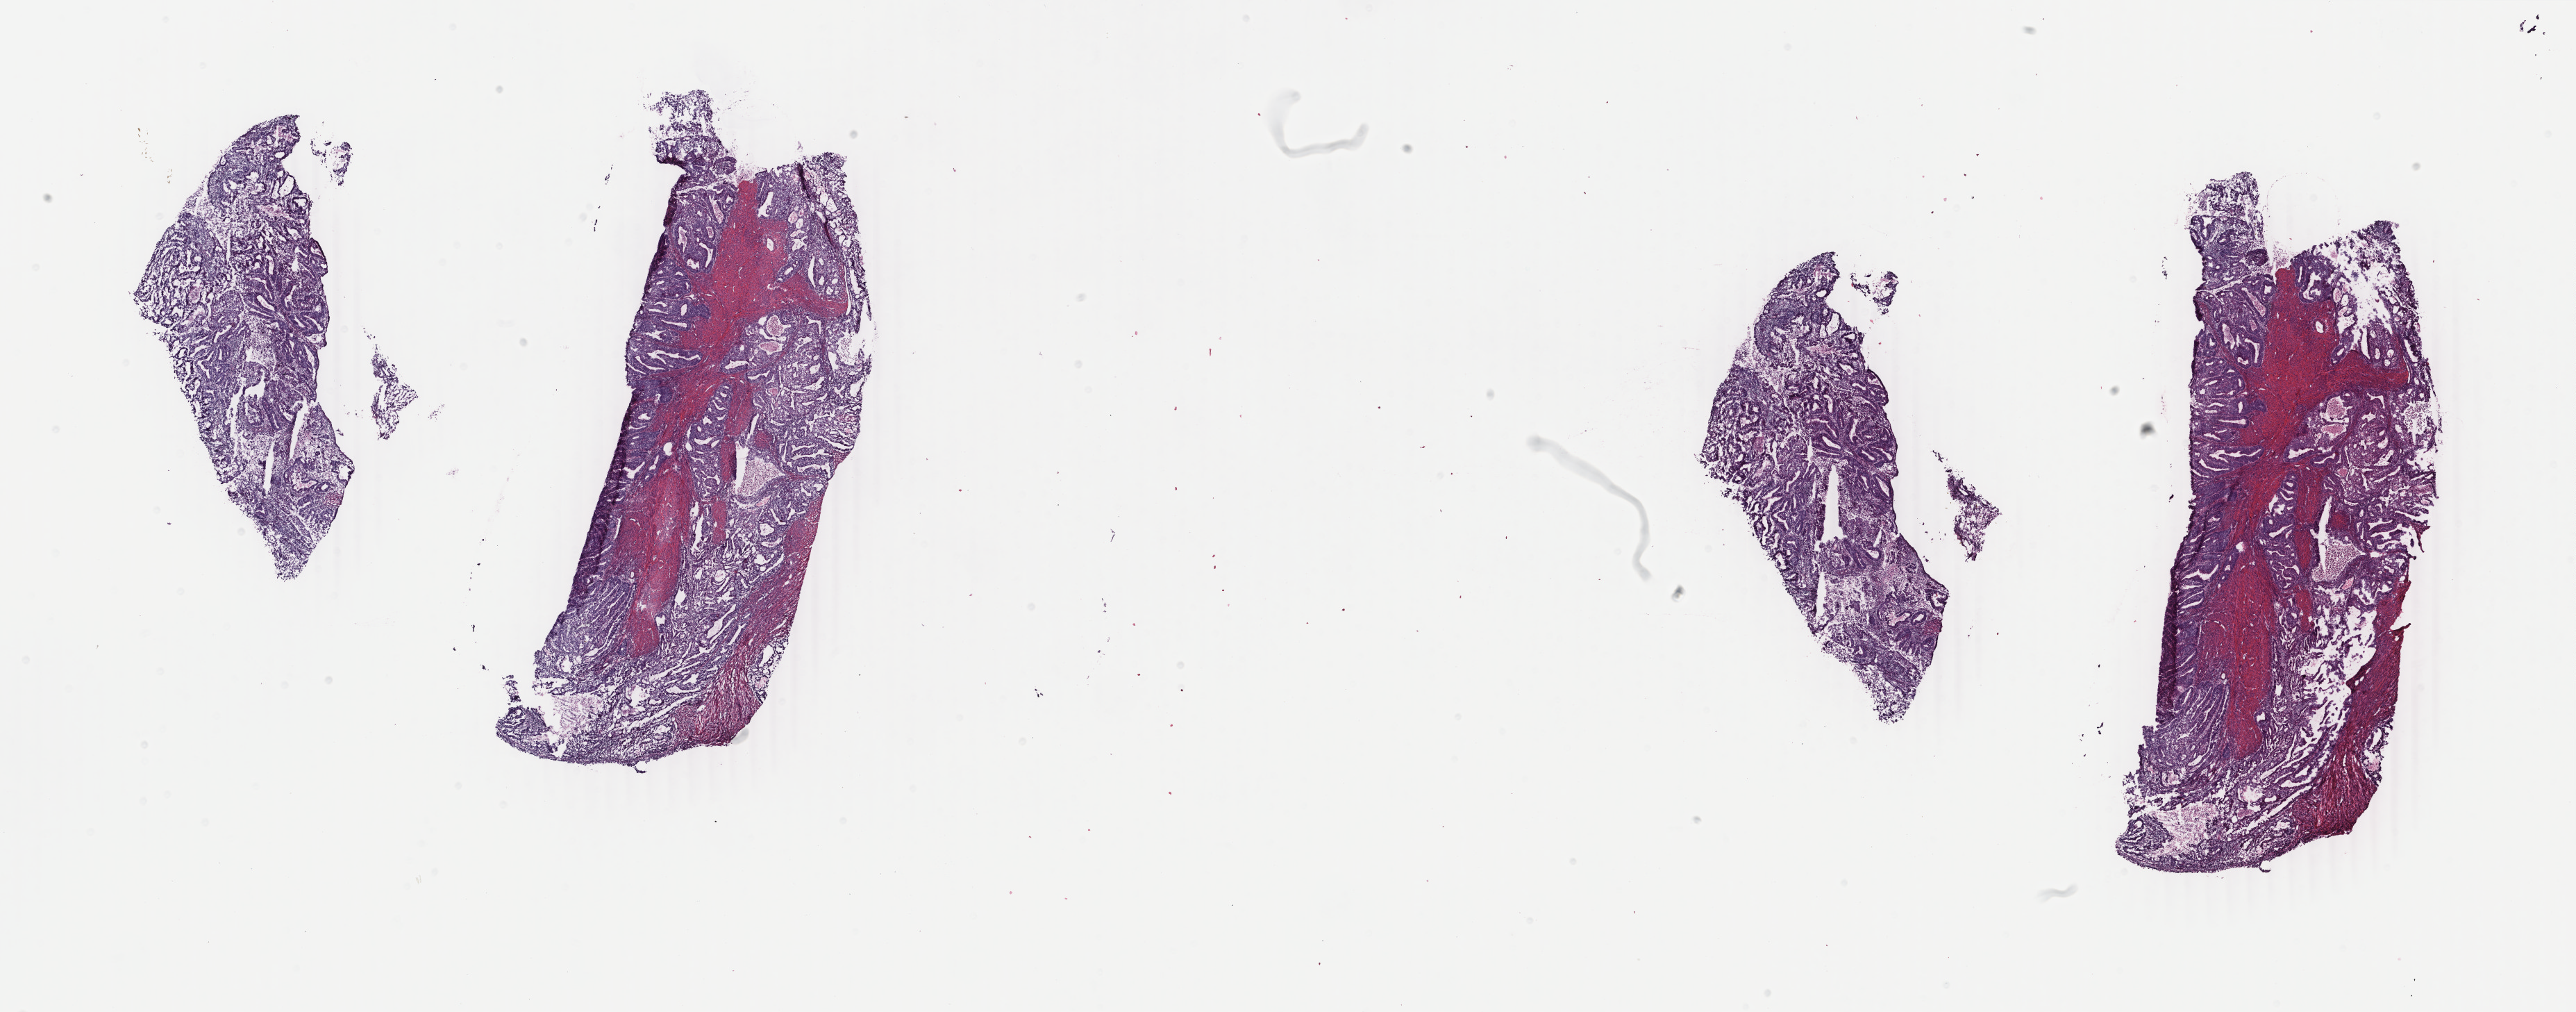
H&E-stained whole-slide image, whole scanned area (about 29.5 x 11.6 mm) shown as a low-resolution overview, frozen section, uterus, primary tumour sample. Female patient; age at initial diagnosis 68 years. Histologic grade: G2 (moderately differentiated). Pathologist review of this section (percent, as recorded): tumour cells 70%, tumour nuclei 70%, normal cells 5%, stromal cells 20%, necrosis 5%. Inflammatory infiltration, as recorded: lymphocyte infiltration 30%, monocyte infiltration 20%, neutrophil infiltration 30%.
• FIGO stage: IB
• diagnosis: Endometrioid adenocarcinoma, NOS (endometrium)
• lymph nodes positive (case pathology): 0 of 6 examined